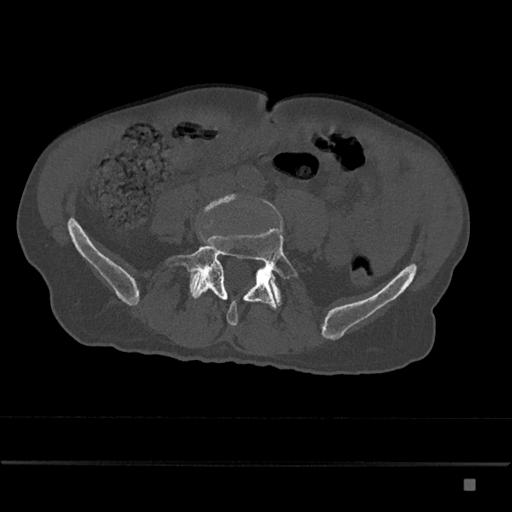
CT including the spine, one axial slice. Position 285 of 797 along the scan axis. 120 kVp. Bone window (W 1800 / L 400 HU). 0.5 mm slice thickness. 512 × 512 image matrix. Male patient, age 72 years. From the clinical record (not read from this slice): primary cancer: prostate.
Outlined on this slice (semi-automatic segmentation, software-assisted and operator-edited):
- L4 vertebra: box from (x=198, y=193) to (x=240, y=217) px
- L5 vertebra: (x=167, y=225)–(x=299, y=326)